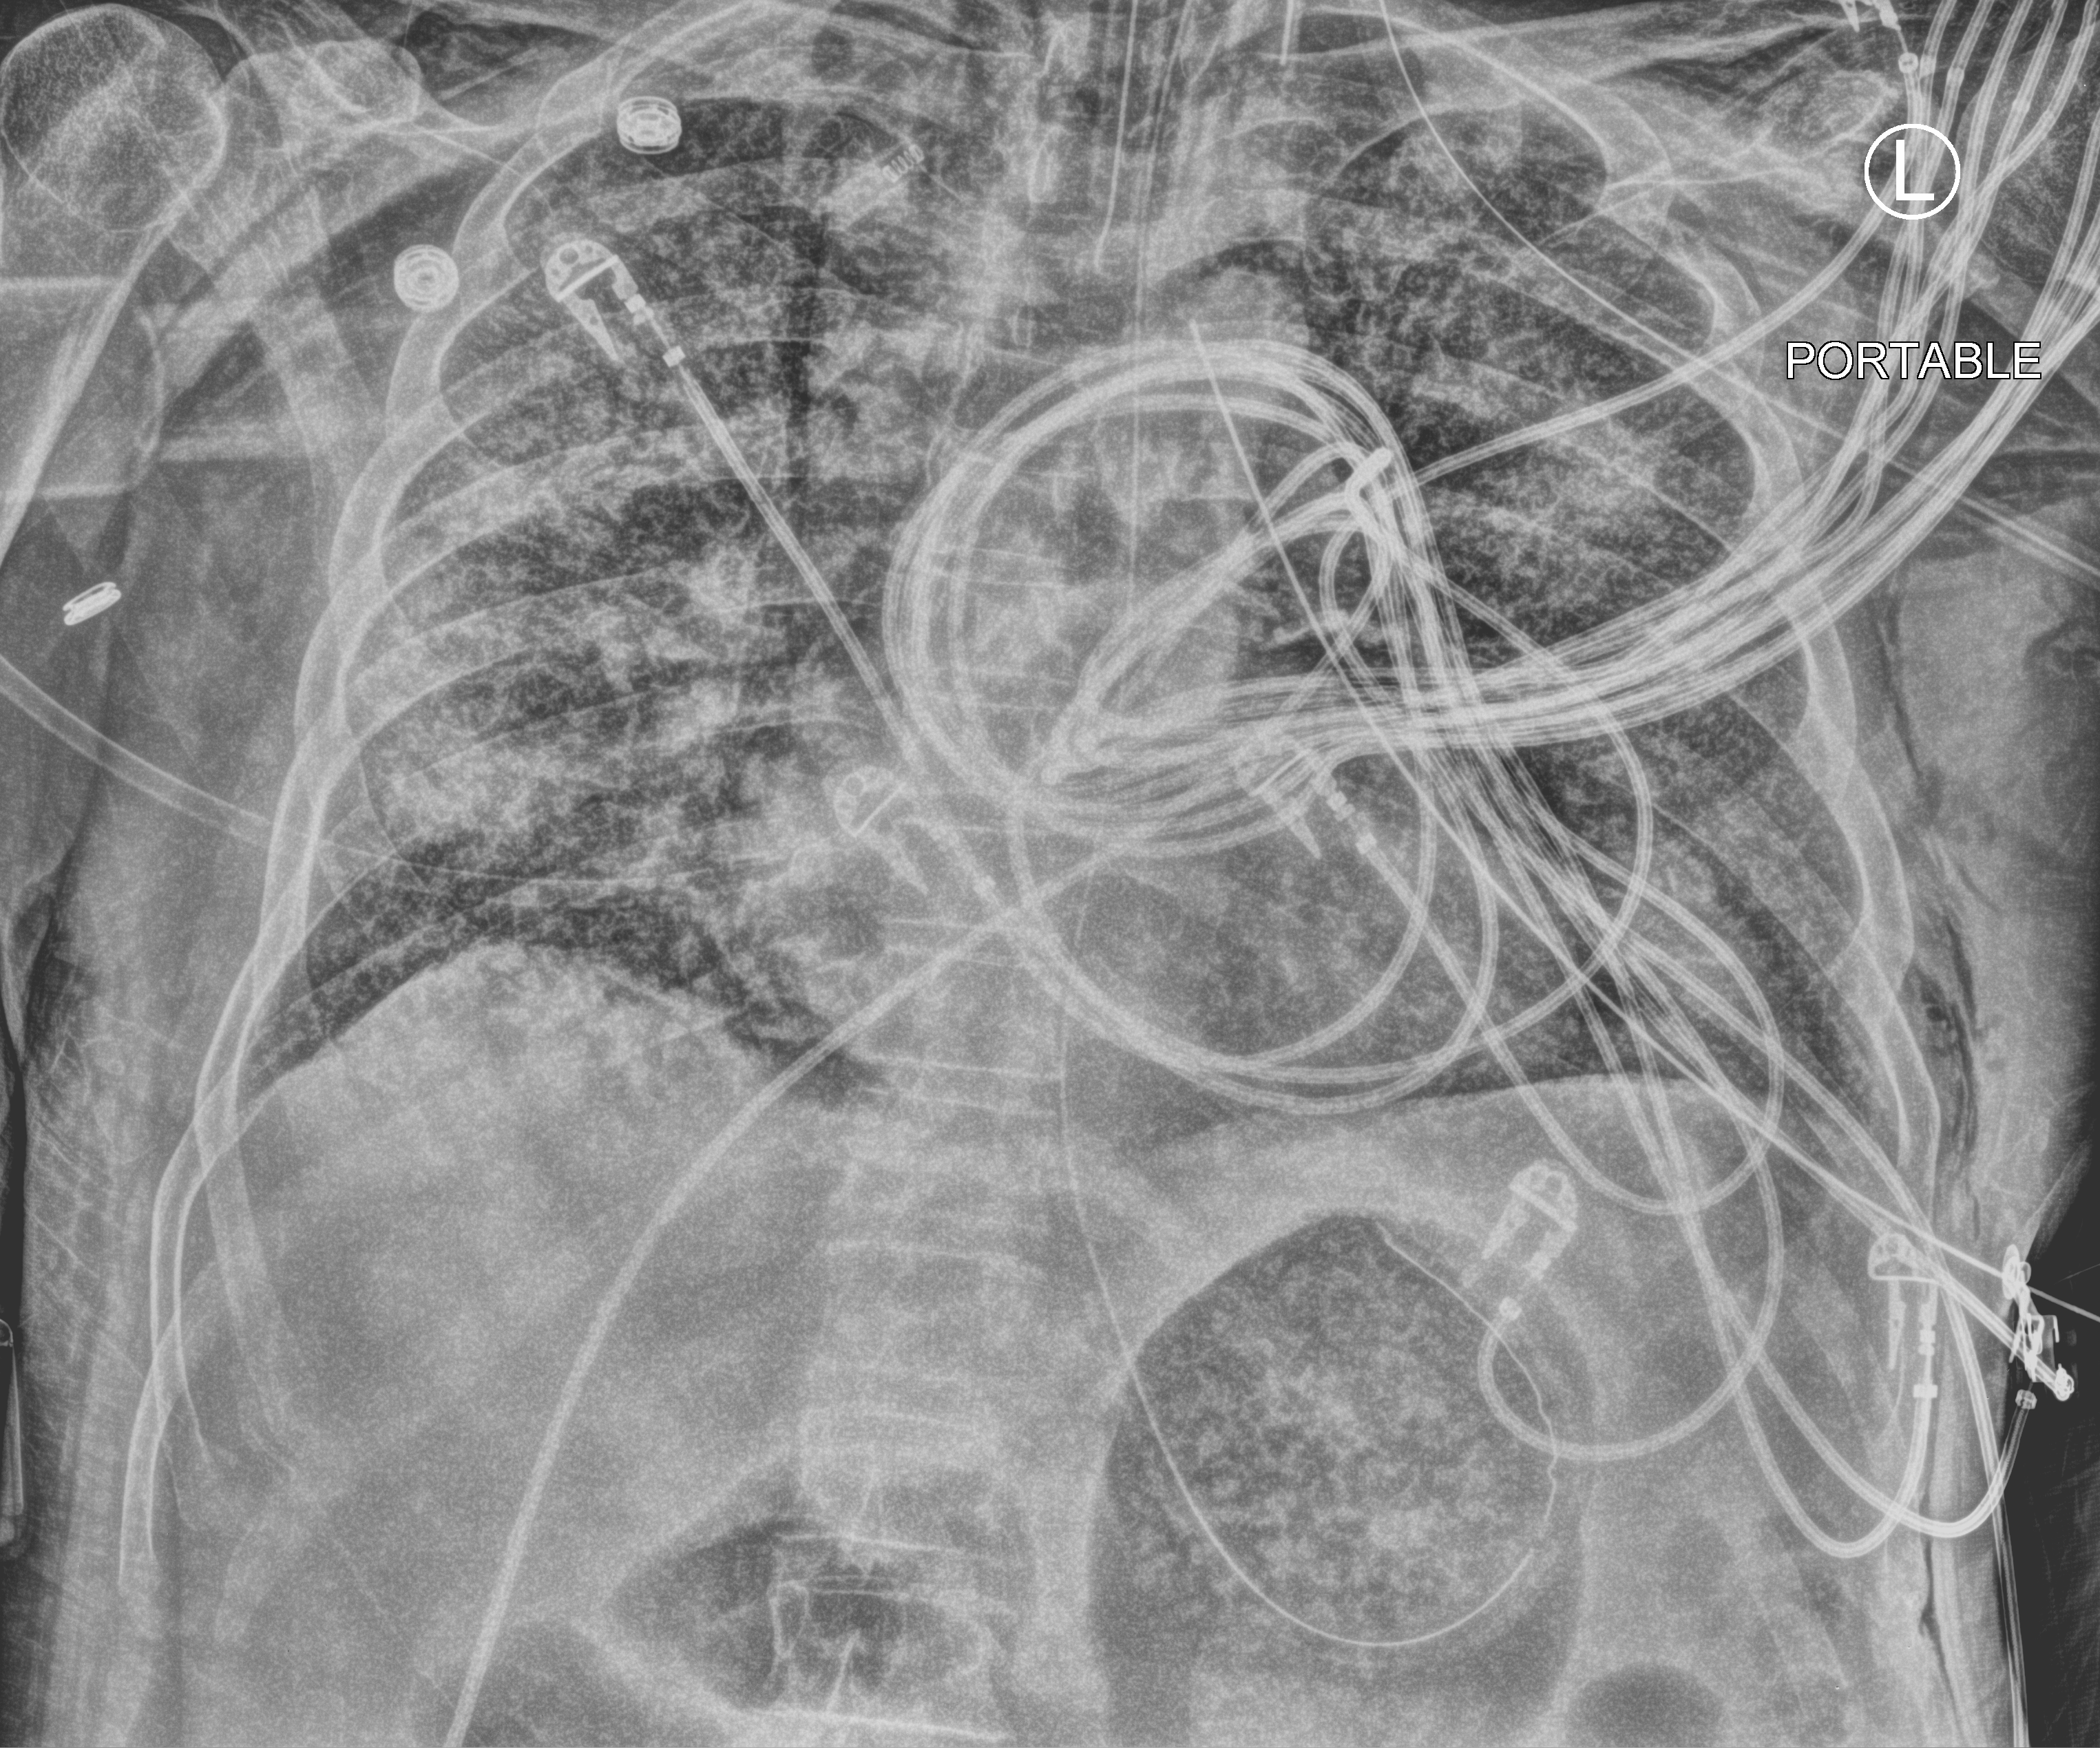
Portable chest radiograph, anteroposterior (AP) projection. Male patient hospitalised with COVID-19, age 60–74 years.
From the hospital-stay record, not from the radiograph (when in the stay this image was taken is not recorded):
- admitted to intensive care during this hospital stay: yes